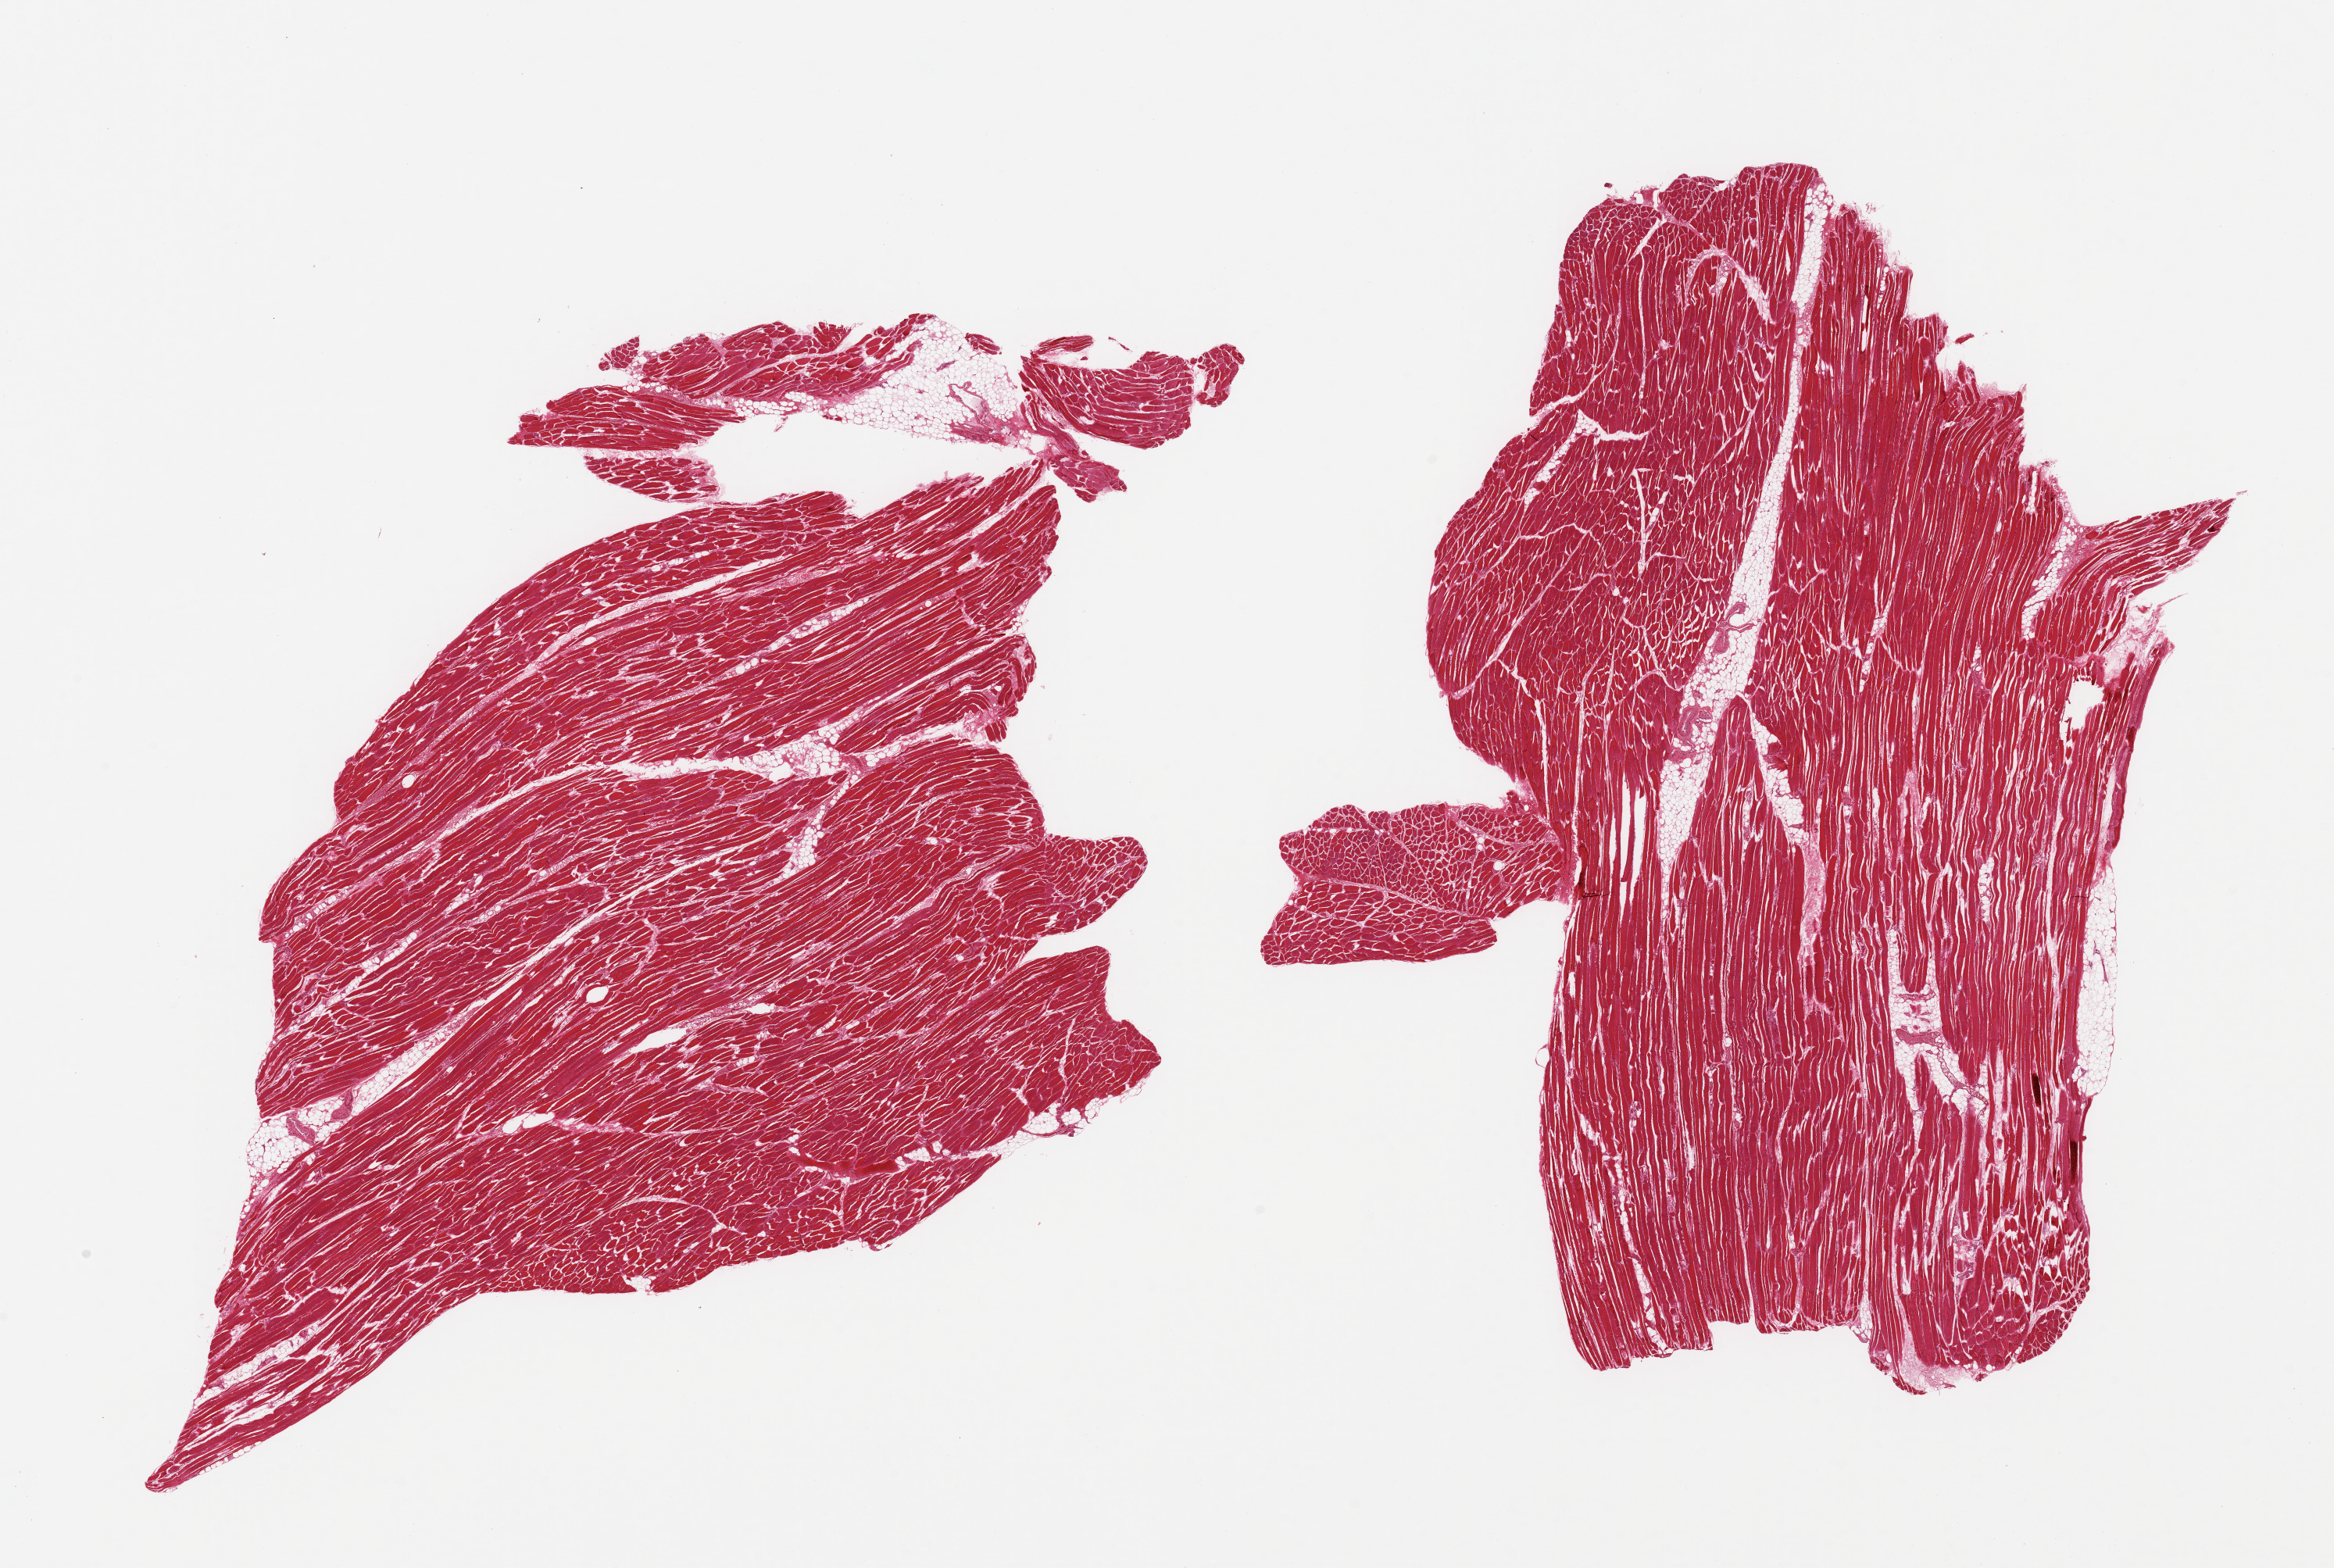
H&E whole-slide image, brightfield, low-resolution overview of the scanned area, about 23.6 x 15.9 mm (from a 20x scan). PAXgene-fixed paraffin-embedded (PFPE) section. Sampled site (target tissue): skeletal muscle. Donor tissue sample. Male donor.
• pathologist's review note for this sample: 2 pieces; ~20% internal fat